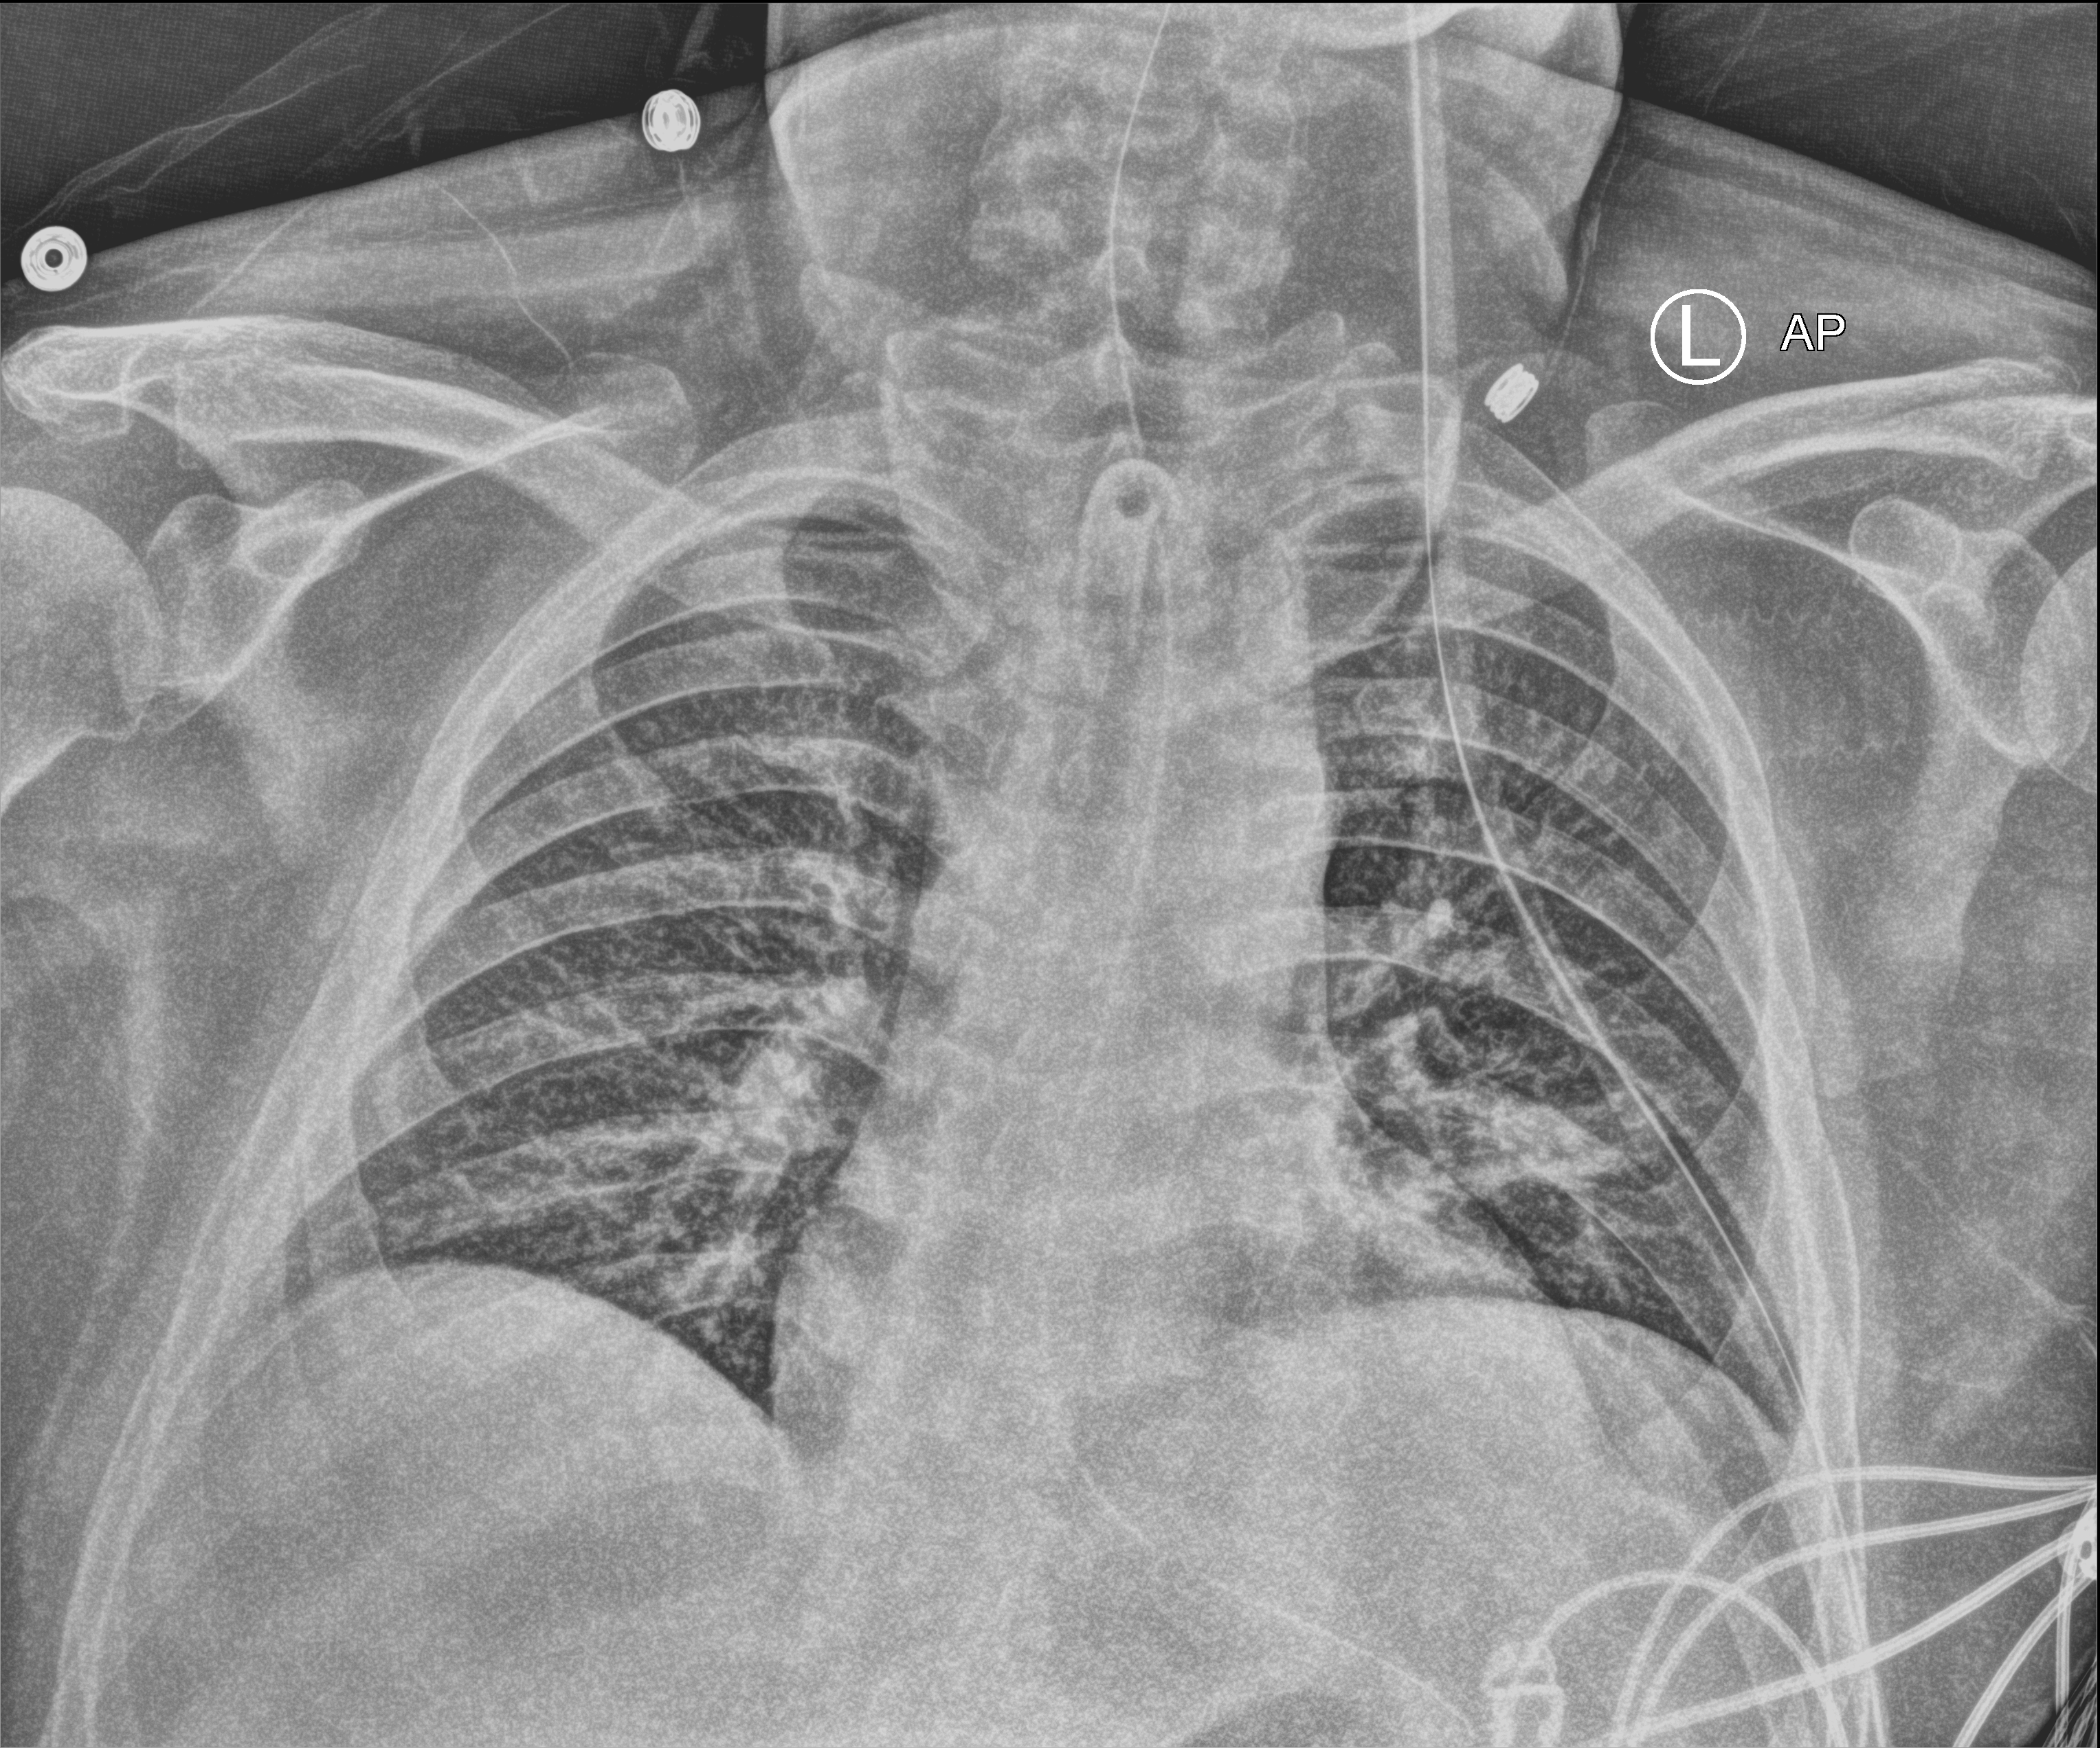
Portable chest radiograph, anteroposterior (AP) projection. Patient hospitalised with COVID-19; male, aged 18–59 years.
Hospital-stay facts (about this admission, not read from this image; timing relative to this image not recorded):
- mechanically ventilated during this hospital stay: yes